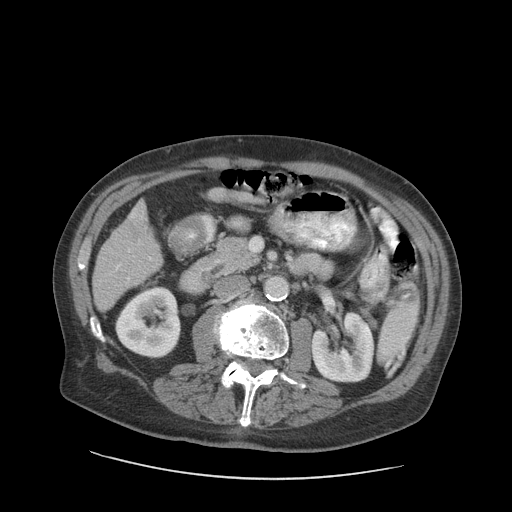
Contrast-enhanced abdominal CT (liver protocol), one axial slice. Position 33 of 89 along the scan axis. Soft-tissue window (W 400 / L 40 HU). 512 × 512 image matrix, field of view 420 × 420 mm. Case-level facts recorded for this patient, not image findings: diagnosis: hepatocellular carcinoma (patient treated with transarterial chemoembolisation; whether this scan precedes or follows treatment is not stated here); TNM stage (as recorded): Stage-I; Child-Pugh class: A; tumour differentiation: moderately differentiated; tumour nodularity: uninodular.
Structures marked on this image (semi-automatic segmentation, software-assisted and operator-edited):
- liver parenchyma outside the tumour (the mass and vessels are separate outlines, so this box may not span the whole liver): bounding box (x1, y1, x2, y2) in pixels: (92, 201, 162, 312)
- mass: (123, 214, 150, 240)
- liver vessels: (116, 213, 152, 281)